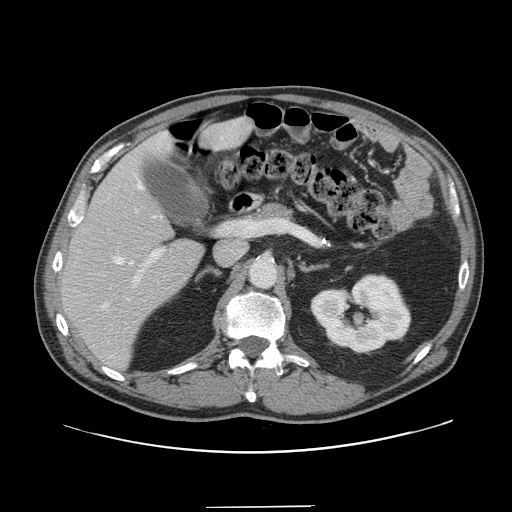
Contrast-enhanced abdominal CT, one axial slice; slice 83 of 139 in the series (ordered by position); 120 kVp; soft-tissue window (W 400 / L 40 HU); 2.5 mm slice thickness; 512 × 512 image matrix, field of view 397 × 397 mm. Male patient, age 64 years. From the clinical record (not read from this slice): diagnosis: colorectal cancer liver metastases, imaged before liver resection; multiple liver metastases: yes; largest metastasis: 3.5 cm.
Outlined on this slice (expert manual segmentation):
- hepatic veins: bounding box (x1, y1, x2, y2) in pixels: (102, 173, 162, 309)
- liver: (62, 120, 249, 368)
- planned liver remnant (the part of the liver to remain after resection): (62, 120, 248, 368)
- portal vein (with intrahepatic branches): (133, 248, 164, 287)